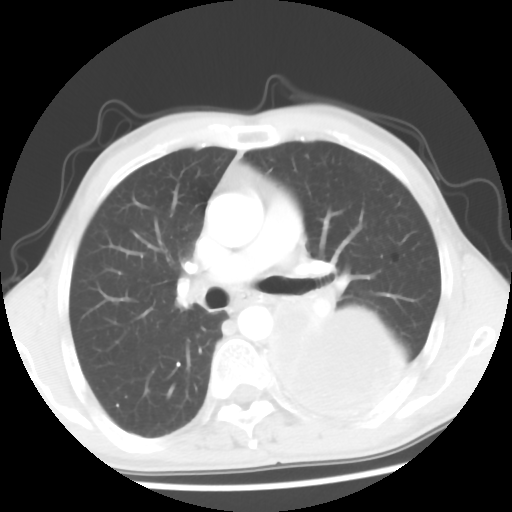
Chest CT, one axial slice; slice 34 of 56 in the series (ordered by position); 120 kVp; lung window (W 1500 / L -600 HU); 5 mm slice thickness; 512 × 512 image matrix, field of view 318 × 318 mm. Patient: male, 60 years. Case-level facts recorded for this patient, not image findings: clinical TNM (as recorded): T4 N0 M0.
Annotated regions visible in this slice (rectangle marked by the reading radiologist):
- lung tumour (recorded histology: squamous cell carcinoma): bounding box [x1, y1, x2, y2] px = [269, 302, 418, 436]